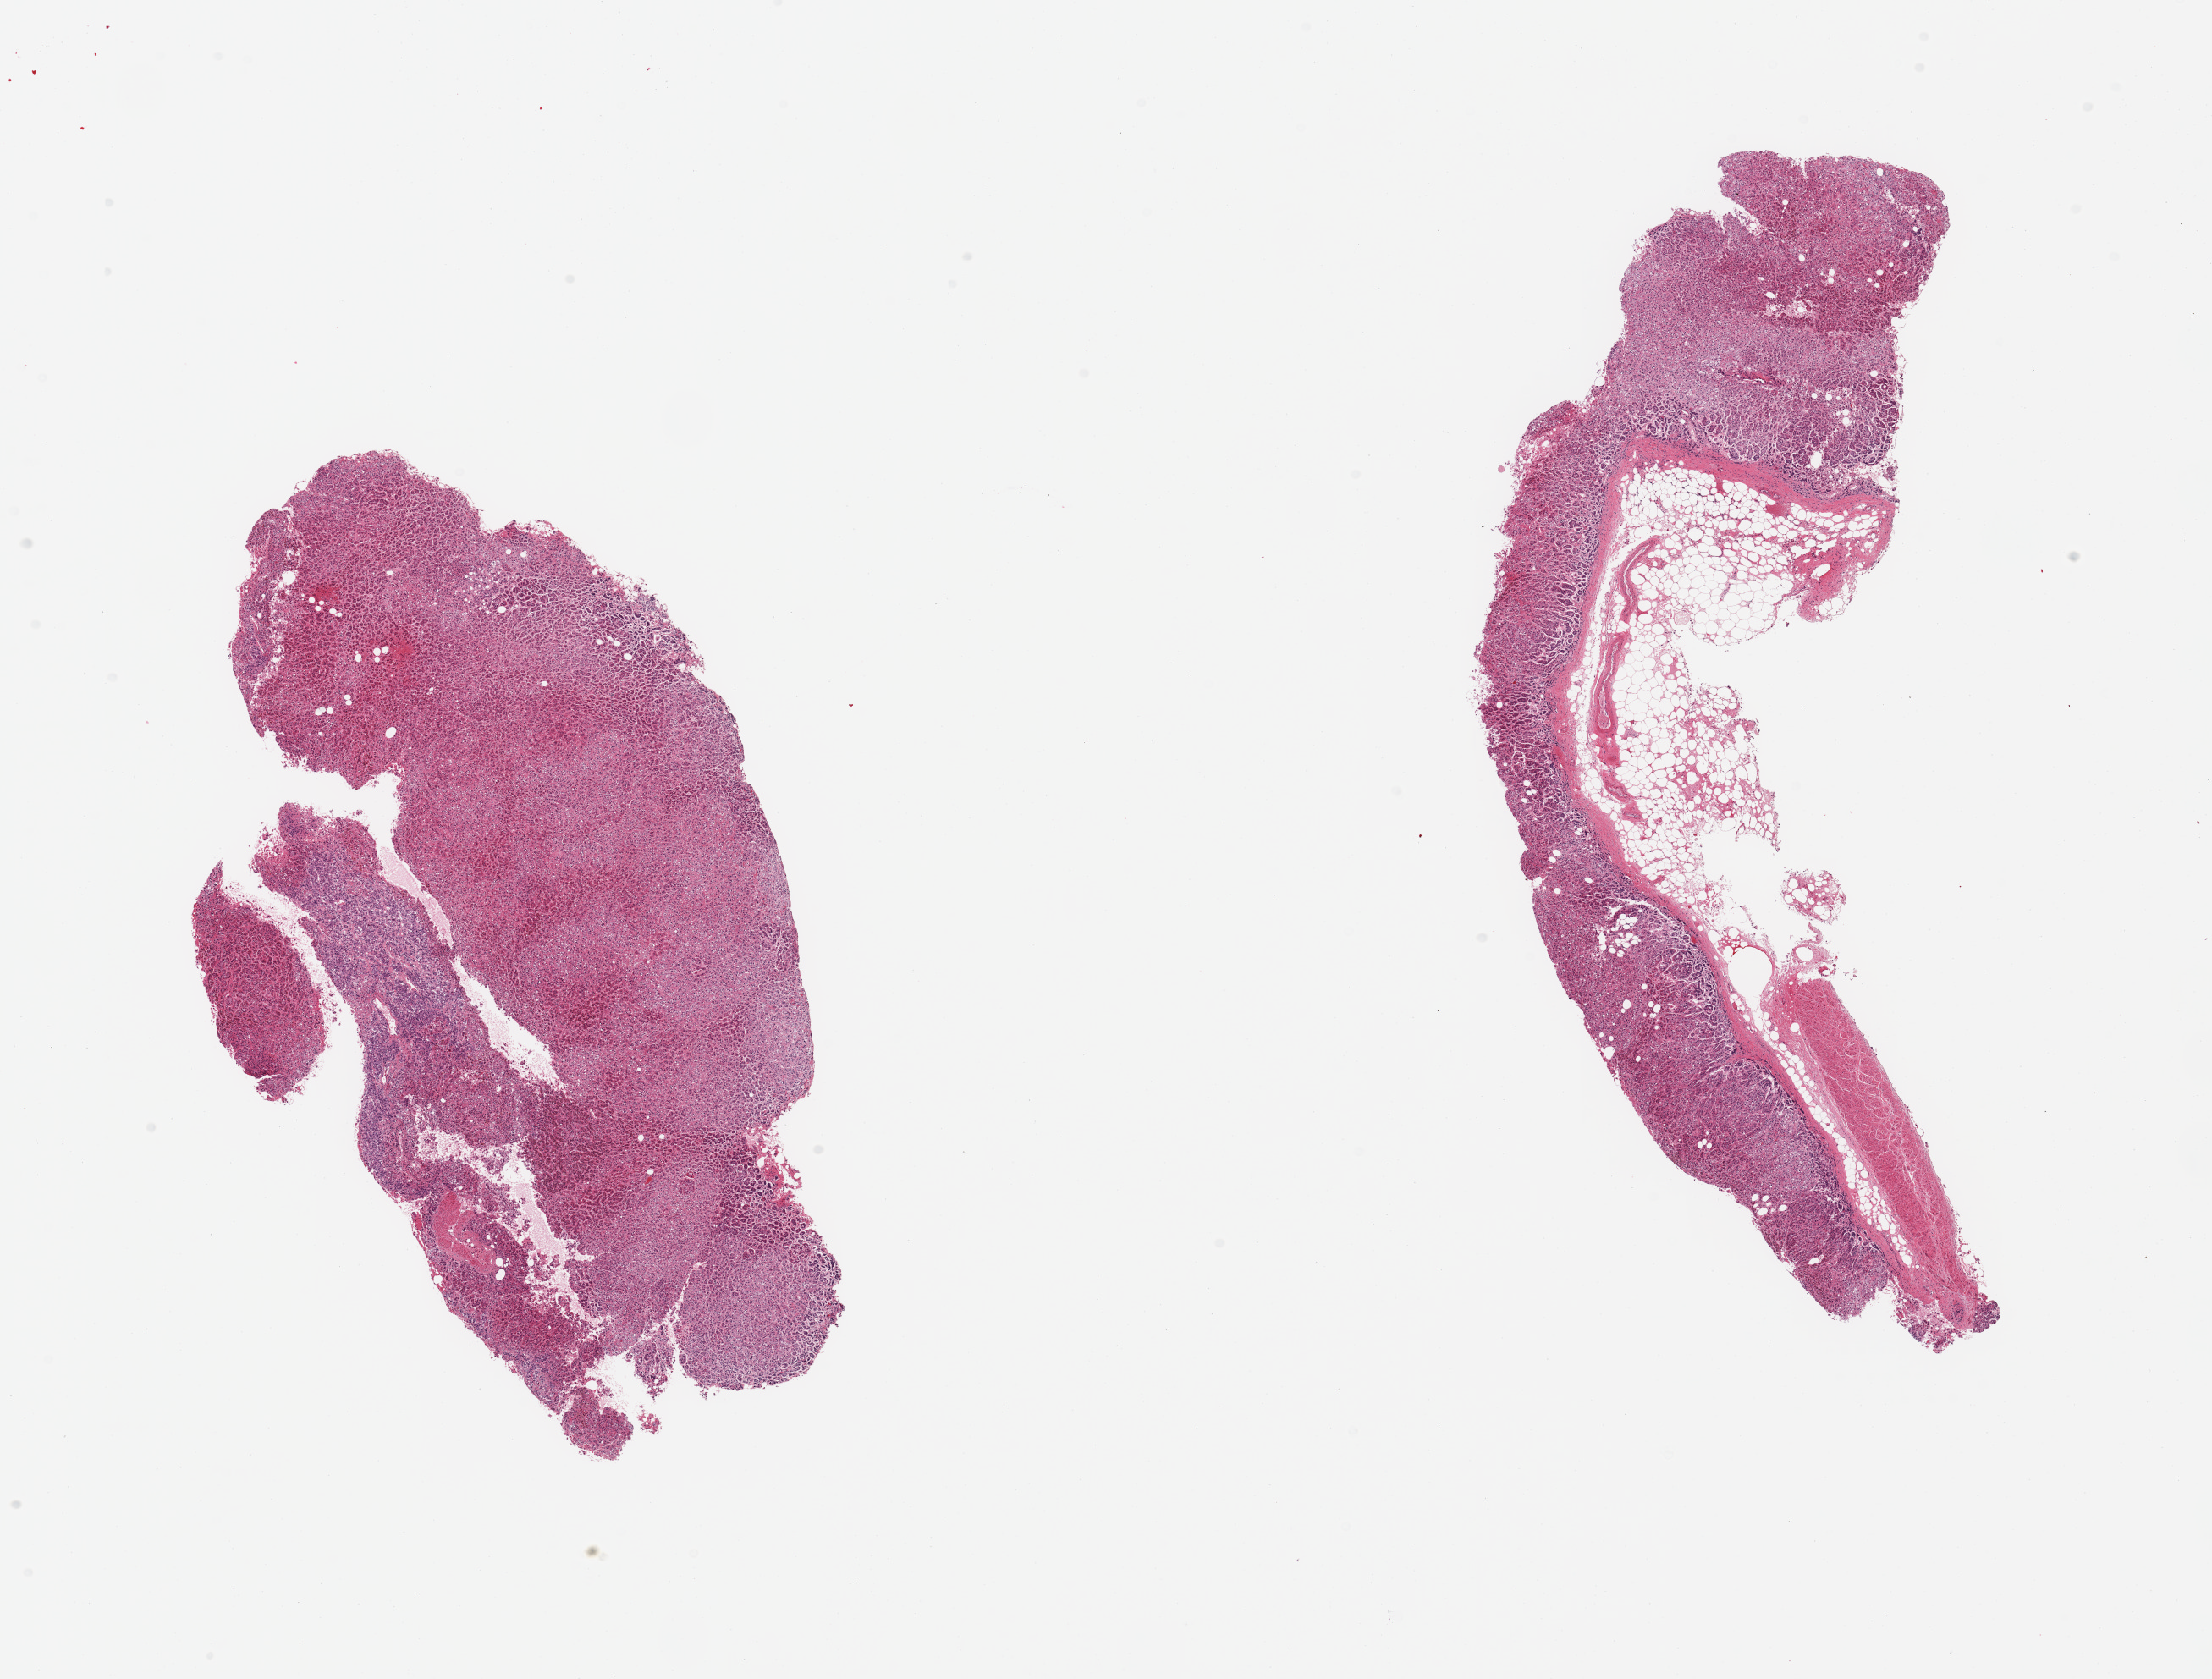
Digitized haematoxylin and eosin-stained section — whole scanned area (about 20.7 x 15.7 mm) shown as a low-resolution overview. PAXgene-fixed, paraffin-embedded tissue. Section of adrenal gland (target tissue). Tissue donor sample. Donor sex: female.
• review note (as recorded): 2 pieces; 1 piece has 40% external fat & vessels